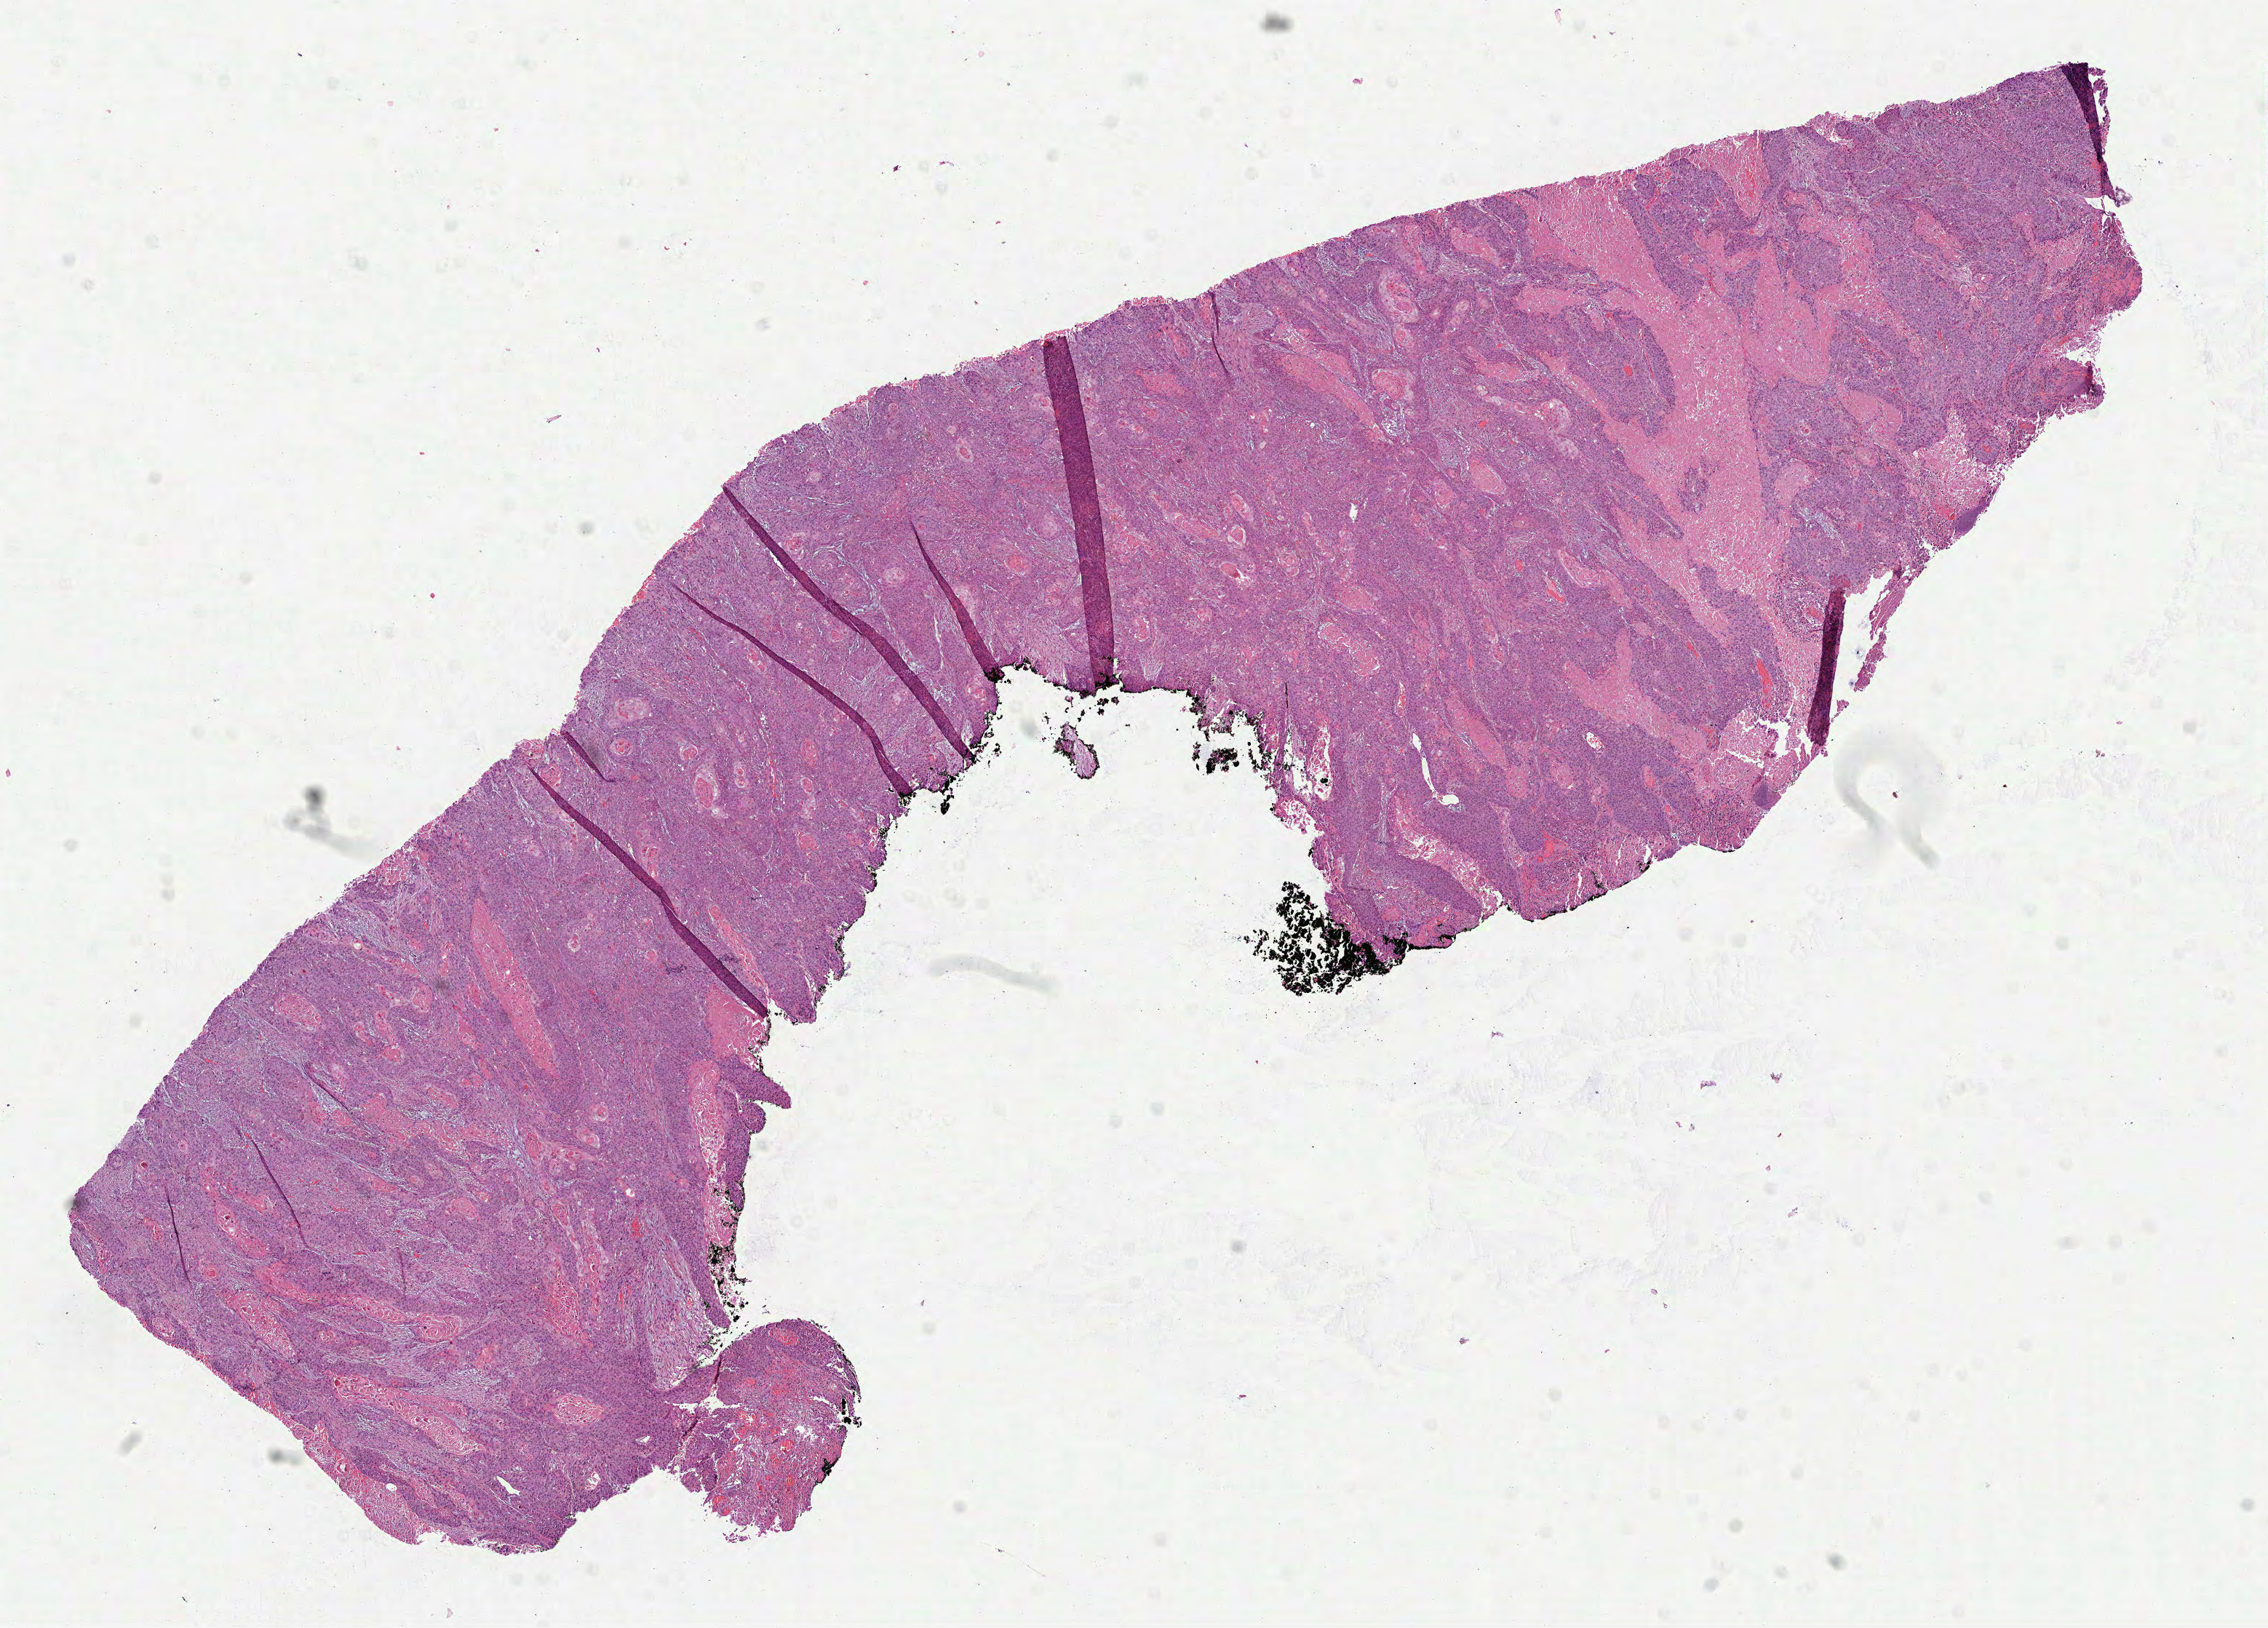
Whole-slide histology image, H&E — a low-resolution overview of the entire scanned area, about 12.6 x 9.0 mm (acquisition: 40x scan); formalin-fixed paraffin-embedded (FFPE) diagnostic section; sample: primary tumour, head and neck. Male patient; age at initial diagnosis 52 years.
Pathologic diagnosis: Squamous cell carcinoma, NOS (floor of mouth, NOS).